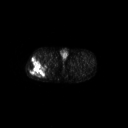
FDG PET of an extremity soft-tissue mass (from a PET/CT study), one axial slice; position 260 of 267 along the scan axis; 3.27 mm slice thickness; 128 × 128 image matrix, field of view 700 × 700 mm. Male patient, age 43 years. Case-level facts recorded for this patient, not image findings: histological type: poorly differentiated synovial sarcoma; grade: high; site of the primary tumour: right buttock.
Annotated regions visible in this slice (expert contour drawn on MRI and transferred to this co-registered scan by the dataset authors):
- gross tumour volume including surrounding oedema: box from (x=27, y=57) to (x=50, y=78) px
- gross tumour volume (mass): (x=27, y=57)–(x=47, y=78)